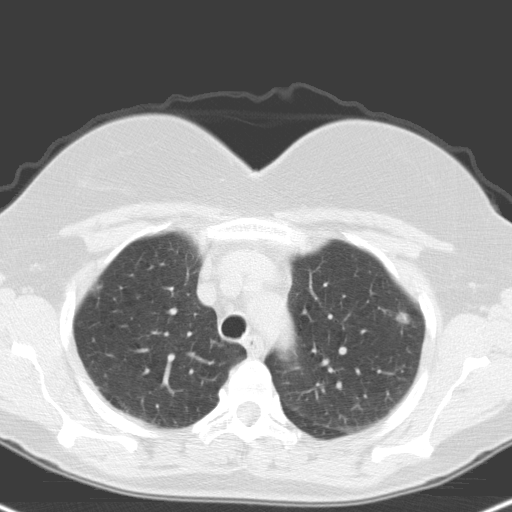
Chest CT (low-dose screening protocol), one axial image; first (baseline) screen; lung window (W 1500 / L -600 HU); slice 26 of 148 in the series; 512 × 512 image matrix. Female participant, aged 59 years at enrolment. Current smoker at enrolment.
Lesion marked by an expert reader, bounding box (x1, y1, x2, y2) in pixels: (384, 293, 428, 340). The screening reader recorded 2 non-calcified nodules or masses ≥4 mm on this exam (right upper lobe, left upper lobe); which of them this box marks is not recorded. Official screen result: positive, change unspecified: nodule(s) >= 4 mm or enlarging nodule(s), mass(es), or other non-specific abnormalities suspicious for lung cancer.